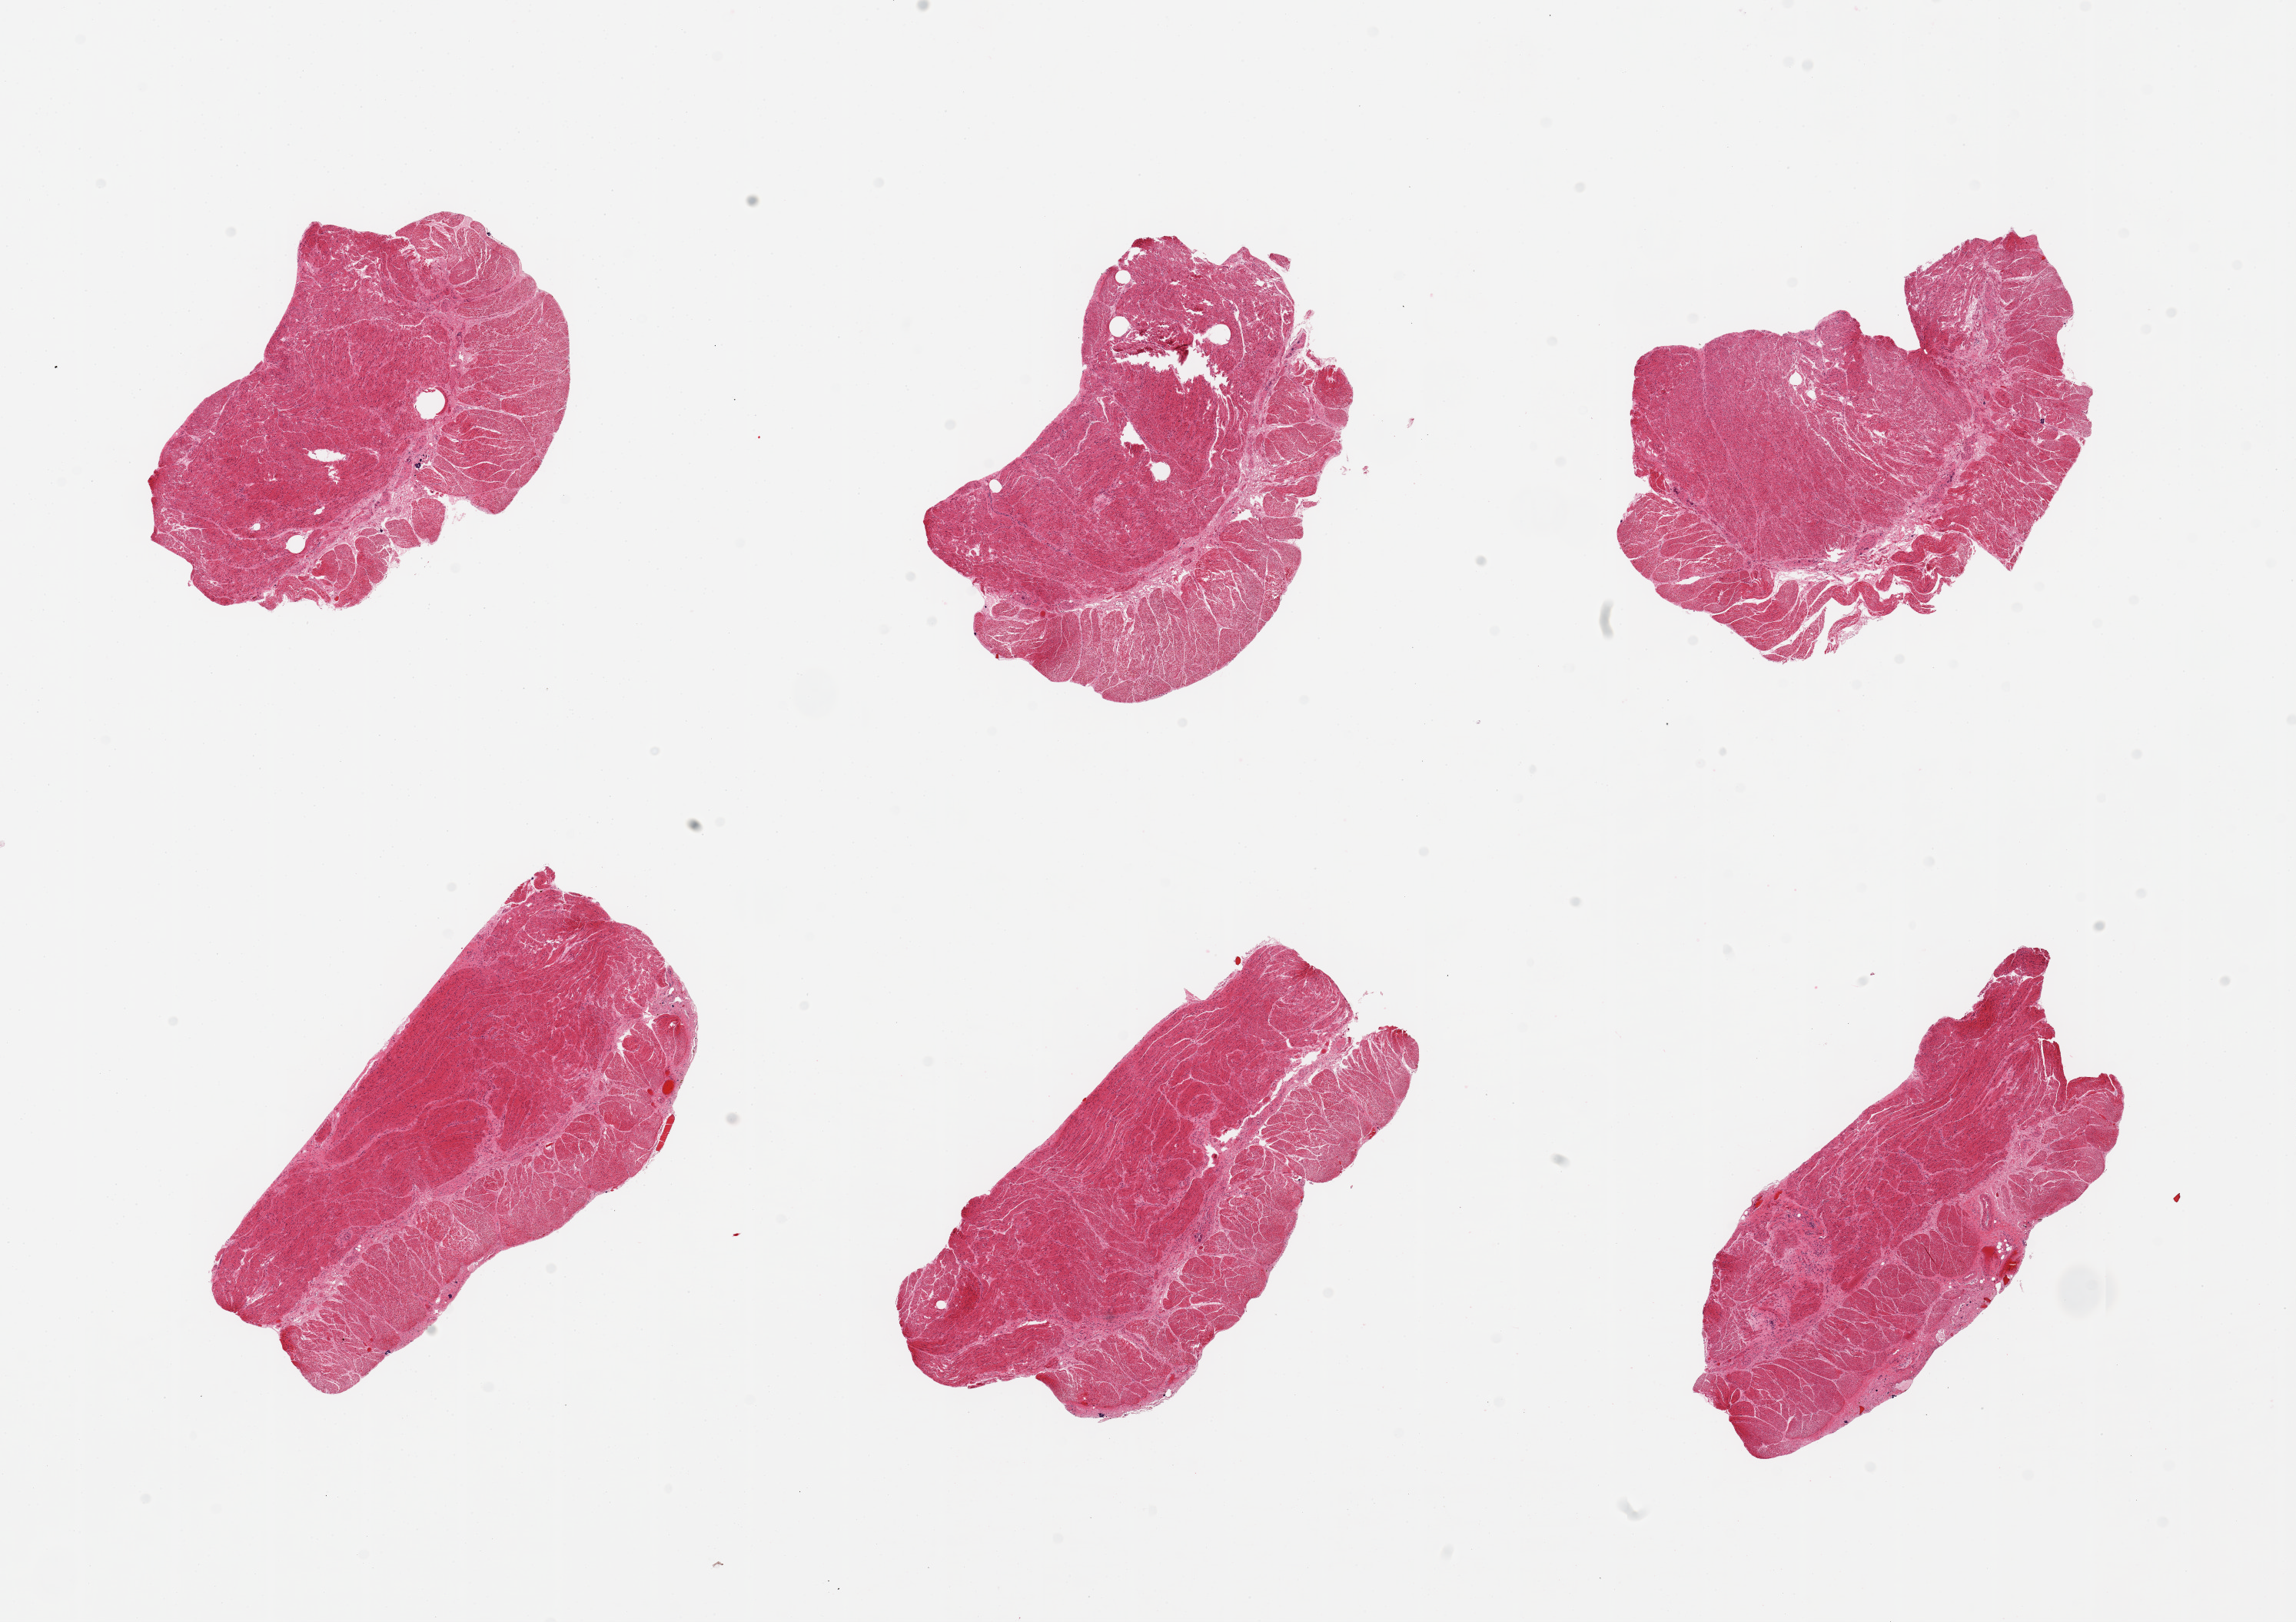
Haematoxylin and eosin whole-slide image — a low-resolution overview of the entire scanned area, about 23.6 x 16.7 mm, PAXgene-fixed, paraffin-embedded tissue, section of gastroesophageal junction (target tissue), donor tissue sample. Donor: male.
Pathologist's review note for this sample: 6 pieces; well trimmed.